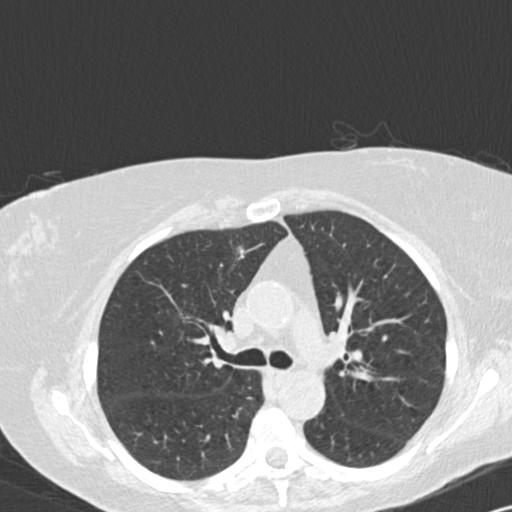
Low-dose screening chest CT, one axial slice; slice 95 of 141 in the series (ordered by position); lung window (W 1500 / L -600 HU); 2 mm slice thickness; 512 × 512 image matrix, field of view 328 × 328 mm.
Annotated regions visible in this slice (manually delineated by an expert):
- lesion 1 (tumor, upper lobe of right lung): box from (x=239, y=247) to (x=245, y=259) px